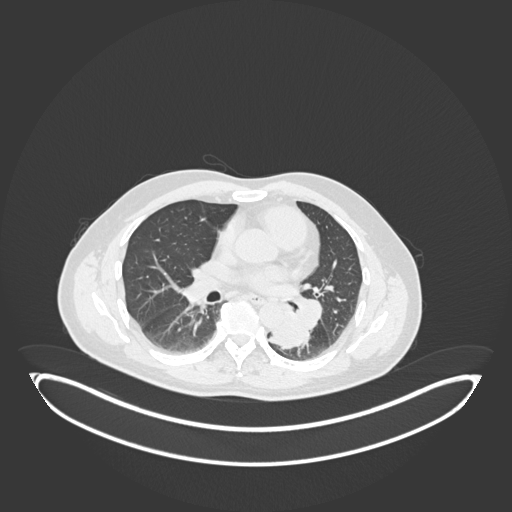
Chest CT, one axial slice. Slice 103 of 258 in the series (ordered by position). Reconstruction kernel B30f. Lung window (W 1500 / L -600 HU). 1 mm slice thickness. 512 × 512 image matrix. Male patient, age 54 years. Case-level facts recorded for this patient, not image findings: clinical TNM (as recorded): T3 N0 M0.
Structures marked on this image (rectangle marked by the reading radiologist):
- lung tumour (recorded histology: squamous cell carcinoma): box from (x=265, y=306) to (x=305, y=347) px